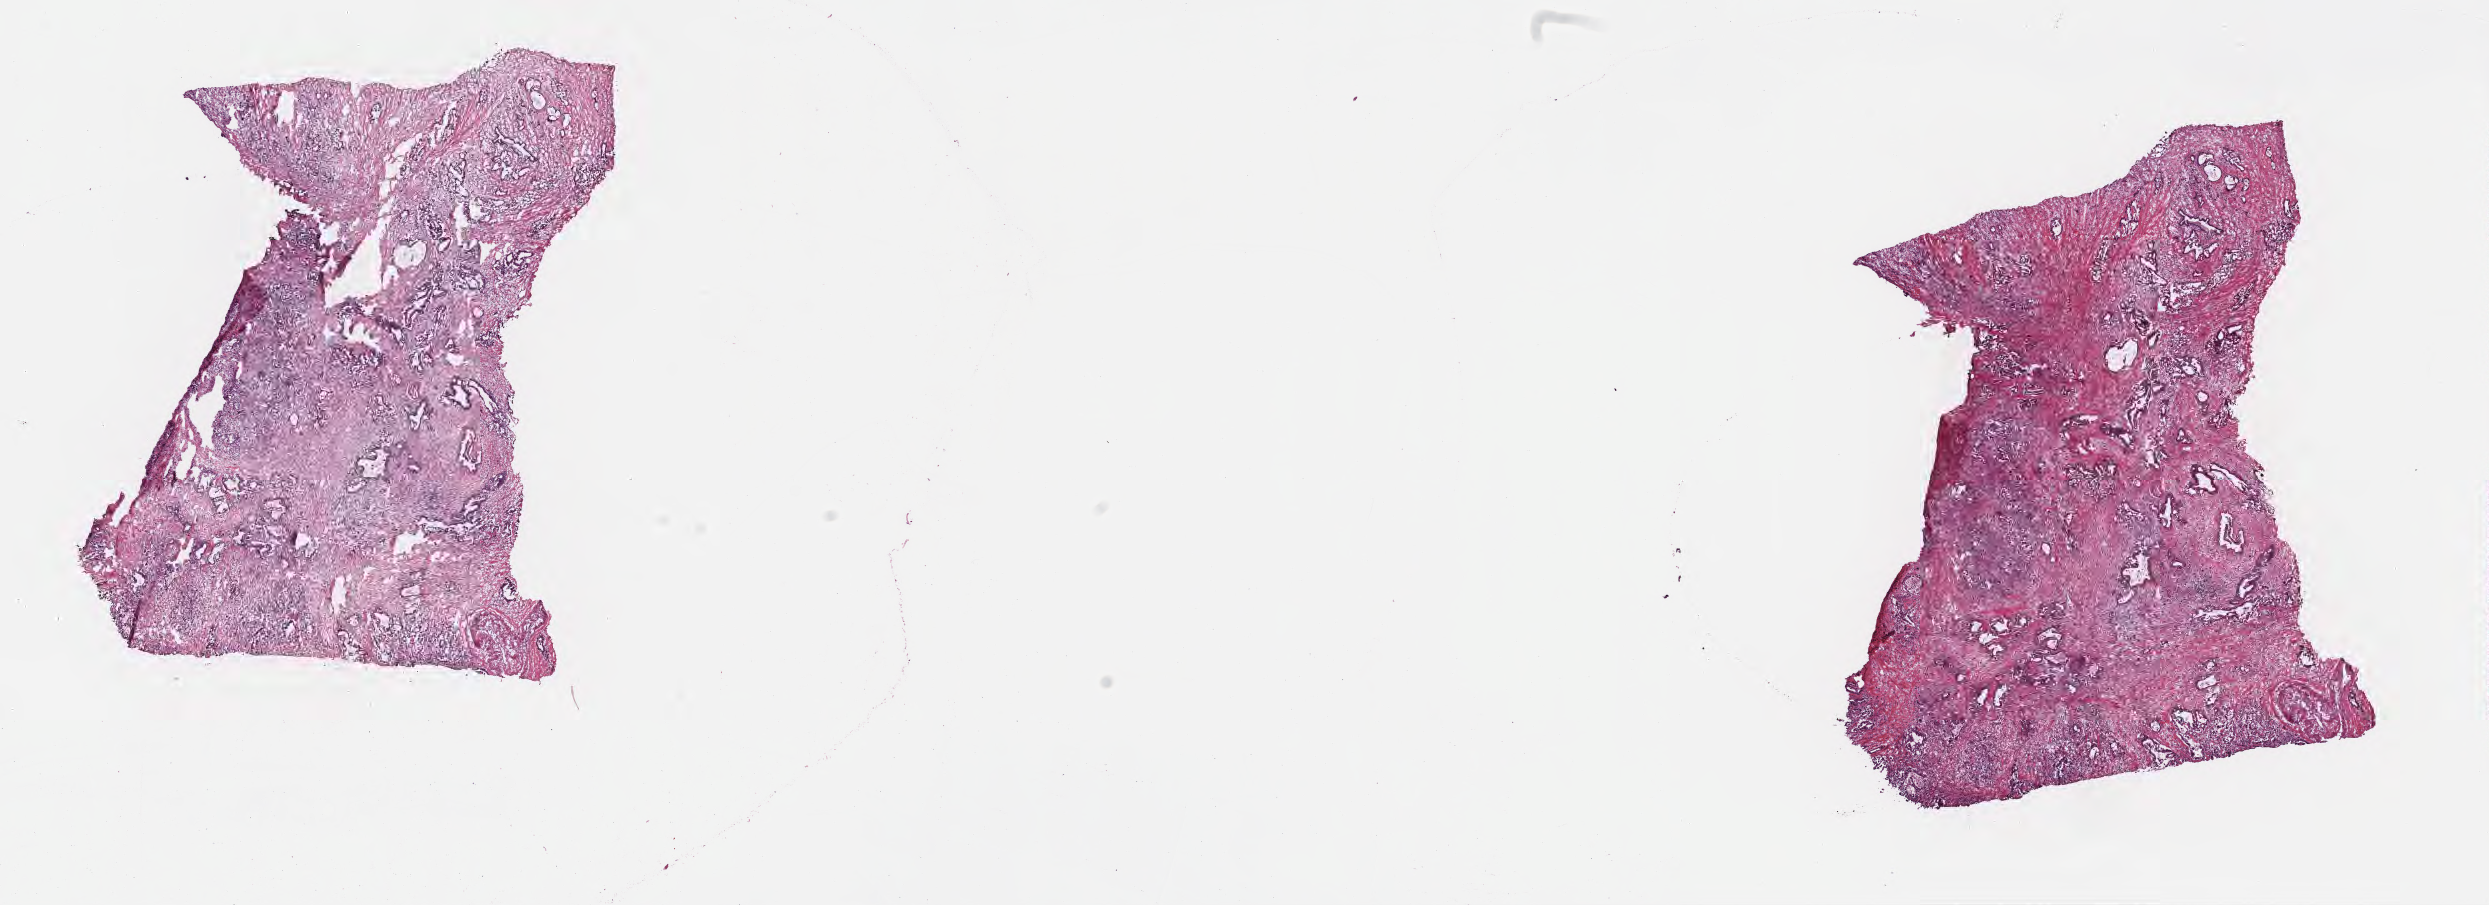
Whole-slide image, haematoxylin and eosin stain, a low-resolution overview of the entire scanned area, about 20.1 x 7.3 mm, cryosection, primary tumor, anatomic site: head of pancreas. Male patient; age at initial diagnosis 67 years. Tumor grade: G3 (poorly differentiated). Slide review estimates, as recorded: tumor cells 75%, tumor nuclei 75%, stromal cells 24%, necrosis 0%, normal cells 1%. Infiltration values recorded for this section: lymphocyte infiltration 6%, monocyte infiltration 1%, neutrophil infiltration 9%.
Section: bottom of the tissue portion. AJCC pathologic stage: Stage IB. Diagnosis: Infiltrating duct carcinoma, NOS.